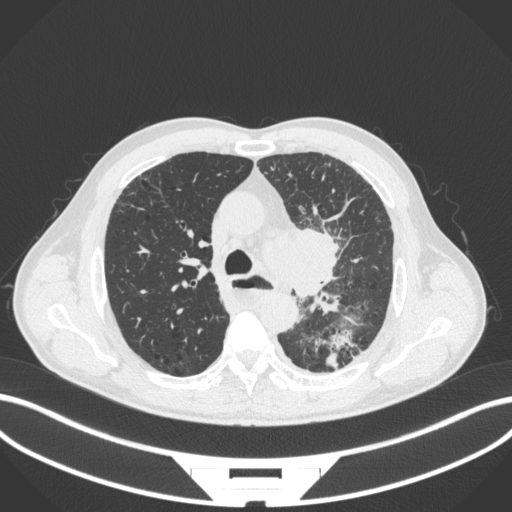
Chest CT, one axial slice; position 263 of 411 along the scan axis; reconstruction kernel B31f; 120 kVp; lung window (W 1500 / L -600 HU); 512 × 512 image matrix, field of view 400 × 400 mm. Patient: male, 57 years. From the clinical record (not read from this slice): clinical TNM (as recorded): T2a N1 M0.
Structures marked on this image (bounding box drawn by a radiologist):
- lung tumour (recorded histology: squamous cell carcinoma): box from (x=254, y=219) to (x=351, y=305) px